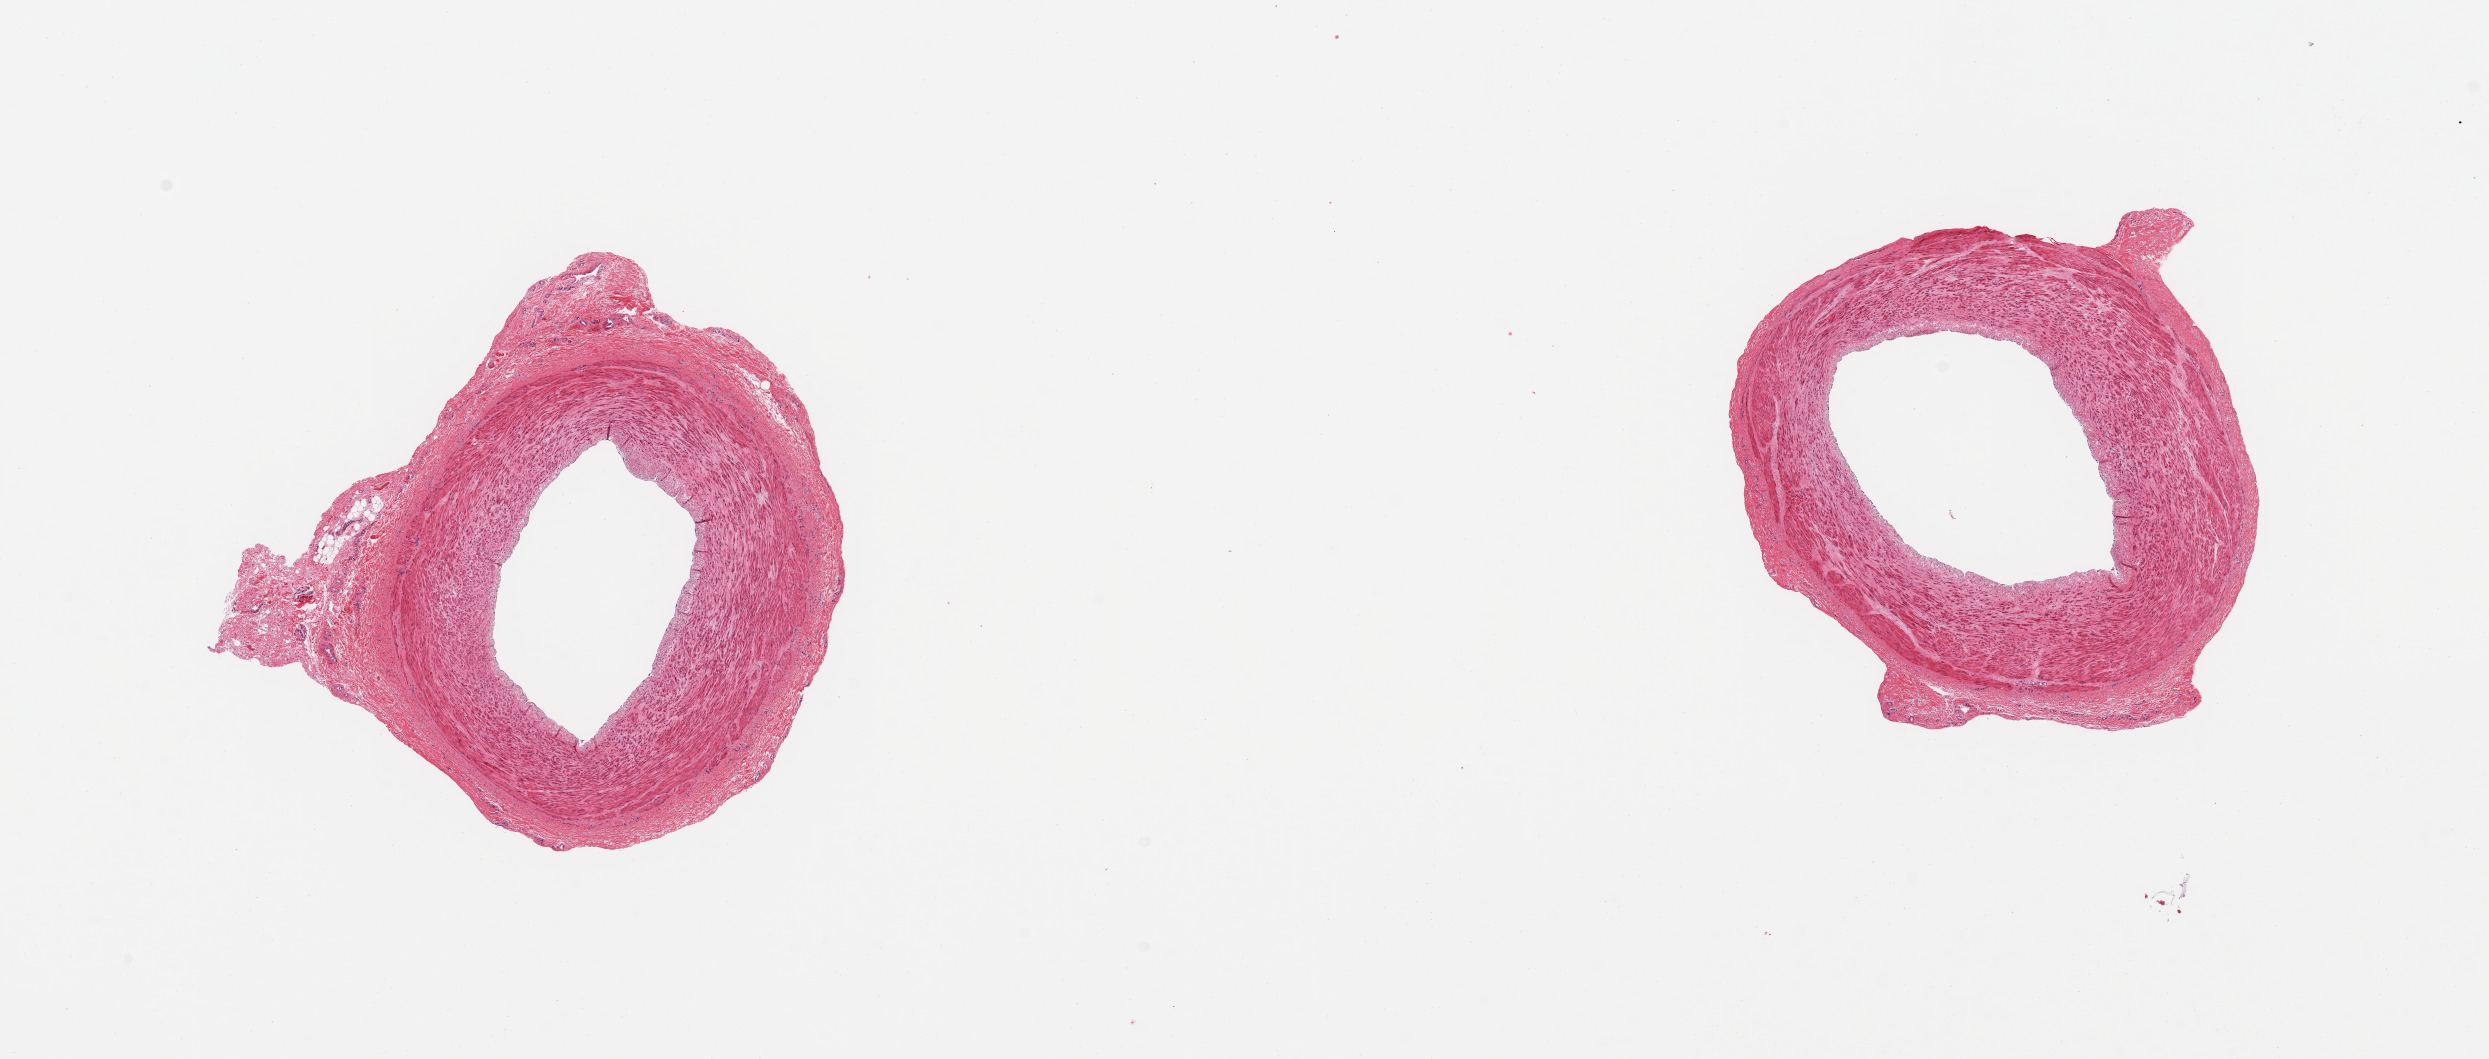
Digitized haematoxylin and eosin-stained section, brightfield, low-resolution overview of the scanned area, about 19.7 x 8.4 mm (acquisition: 20x scan), PAXgene-fixed, paraffin-embedded tissue, target tissue: tibial artery, tissue donor sample. Donor: male.
Pathologist's review note for this sample: 2 pieces; relatively well trimmed.